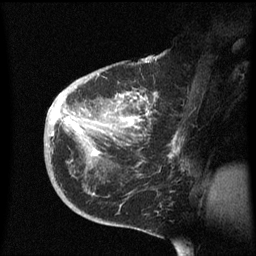
Breast MRI (dynamic contrast-enhanced), one sagittal slice; position 34 of 60 along the scan axis; dynamic contrast-enhanced series, image 2 of 3 at this slice position (ordered by acquisition); 1.5 T; TE 4.2 ms, TR 8.4 ms; 256 × 256 image matrix, field of view 200 × 200 mm. Female patient, age 38 years. Case-level facts recorded for this patient, not image findings: setting: breast cancer imaged before/during neoadjuvant chemotherapy; receptor status: HER2-positive.
Outlined on this slice (semi-automatic segmentation, software-assisted and operator-edited):
- analysis volume of interest (the breast-tissue region the enhancement analysis was run in; not a lesion): bounding box <44,78,186,213> (left, top, right, bottom; pixels)
- tumour enhancement mask (voxels above the 70 % enhancement threshold inside the analysis volume of interest): <52,92,175,155>